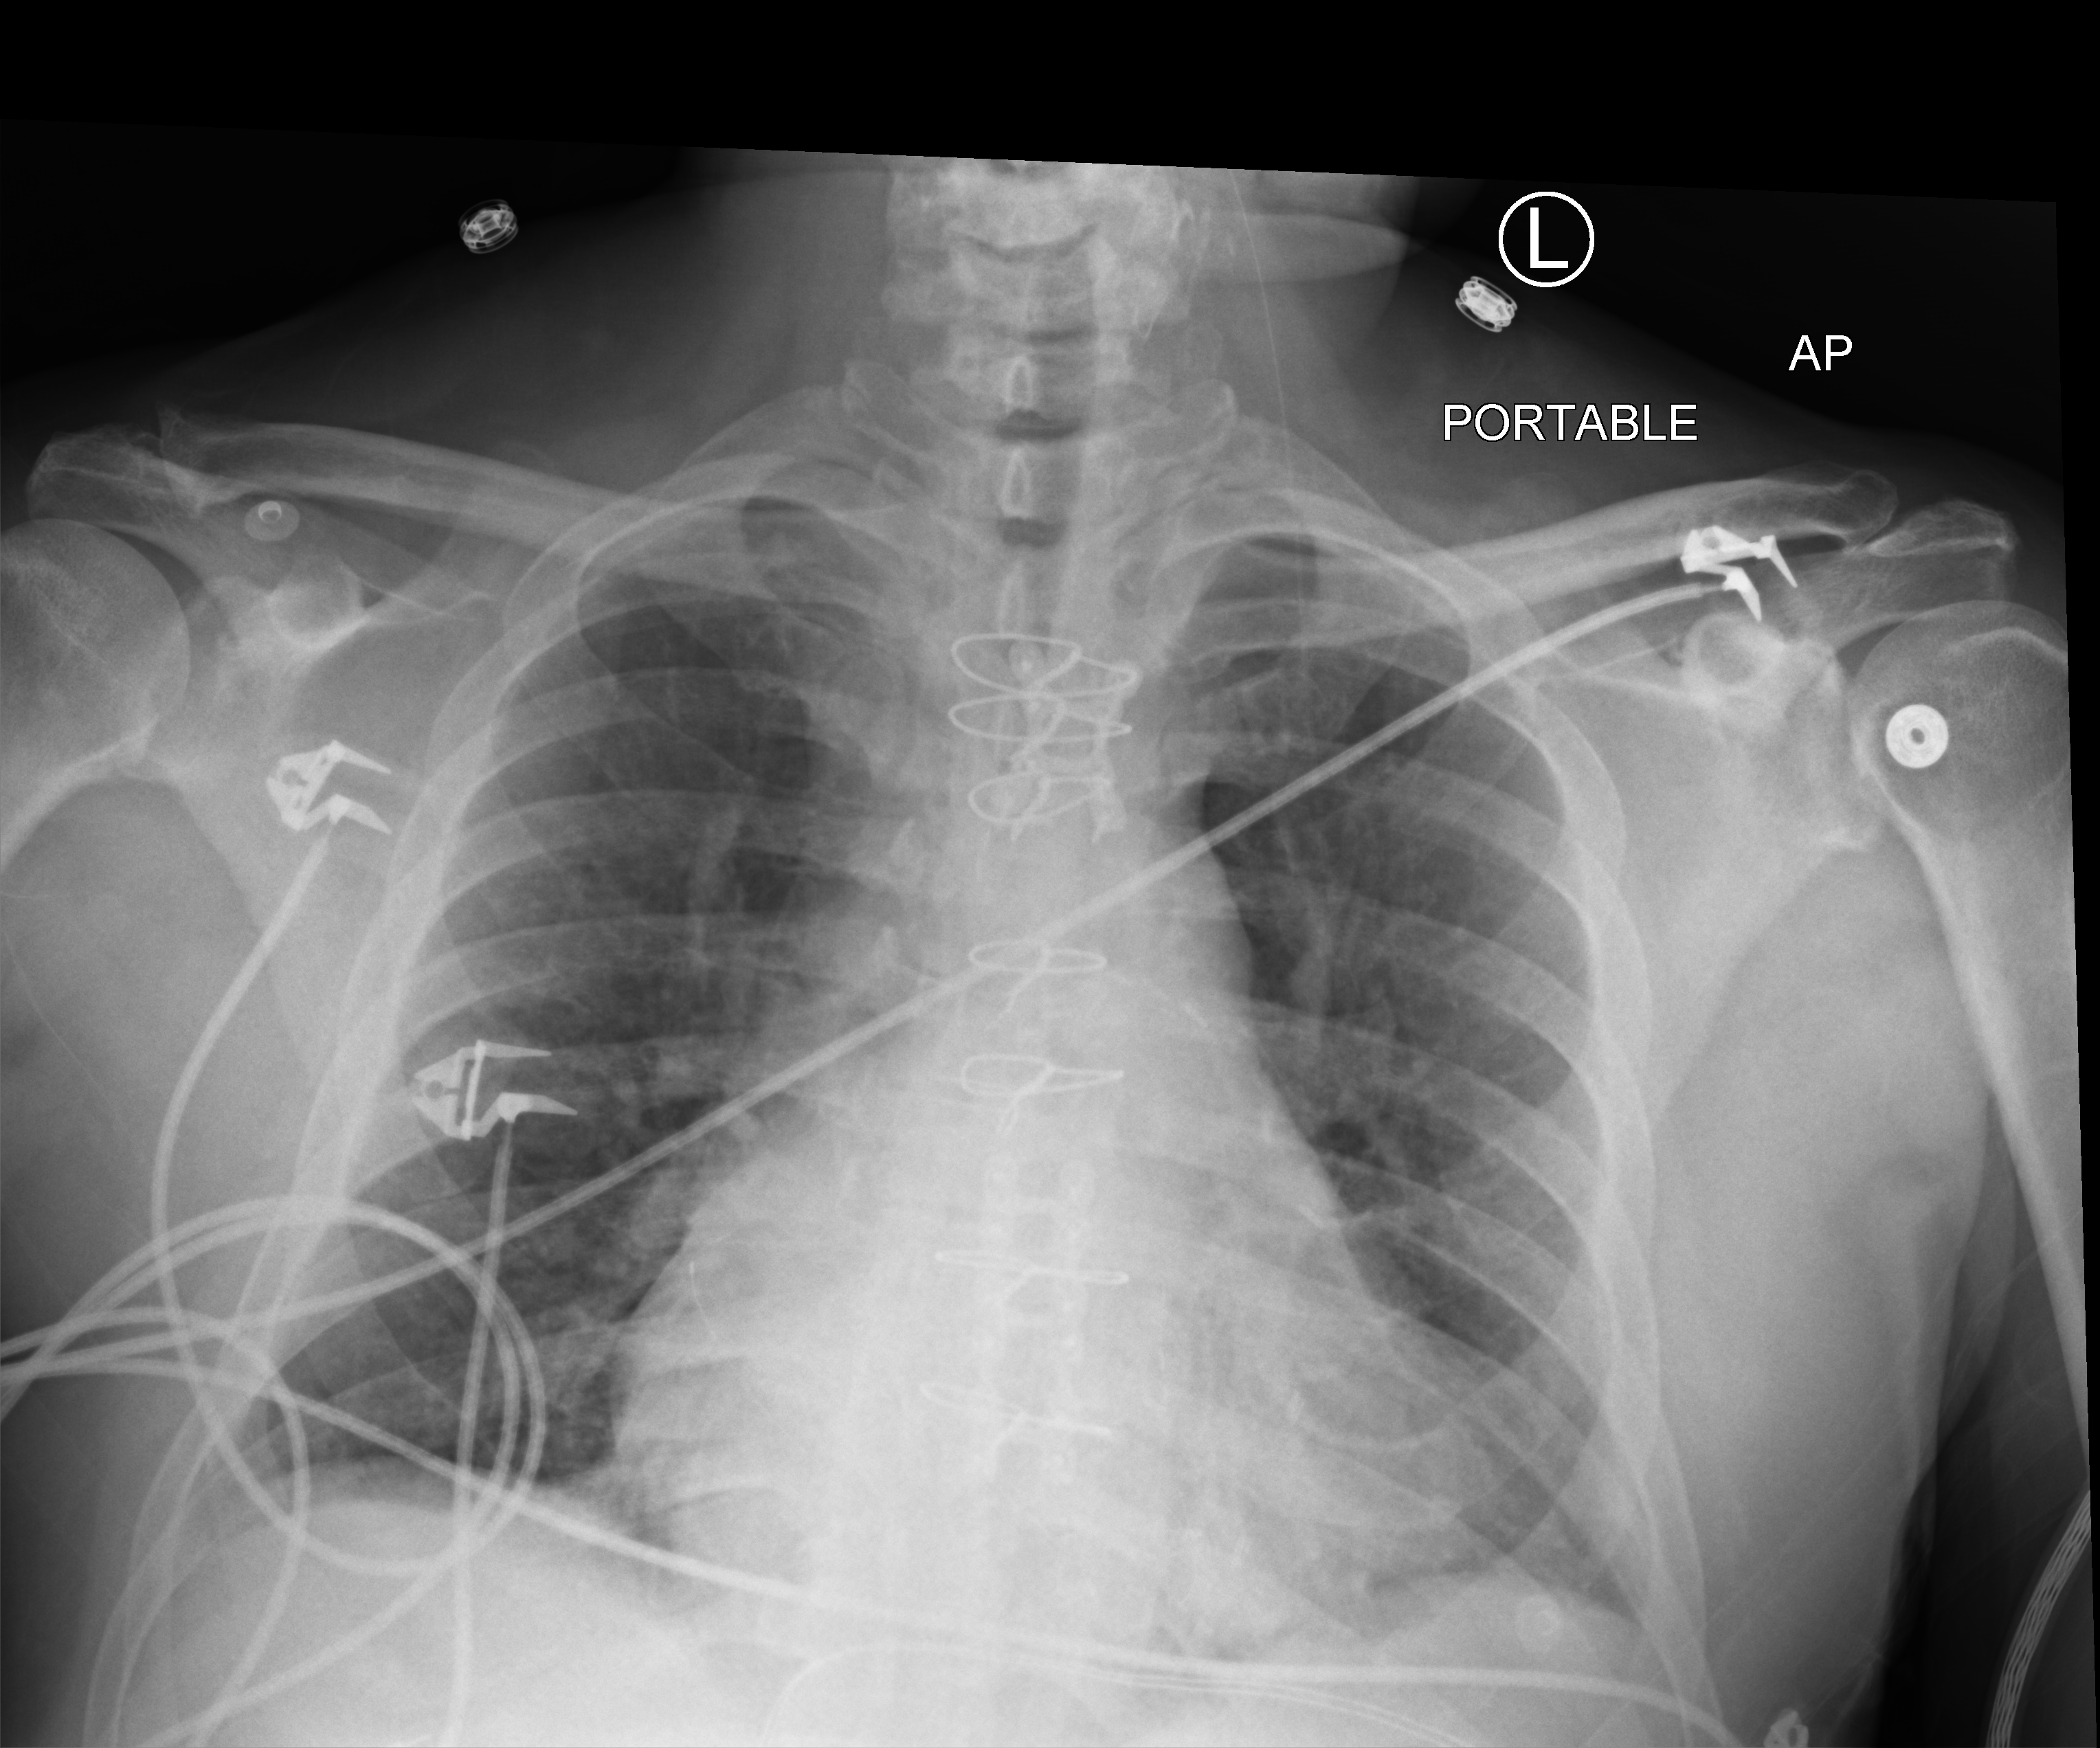
Portable chest radiograph. Male patient hospitalised with COVID-19, age 60–74 years.
Admission-level facts for this patient (not findings on this image; timing relative to this image not recorded): COPD (admission record): no; admitted to intensive care during this hospital stay: no; mechanically ventilated during this hospital stay: no.